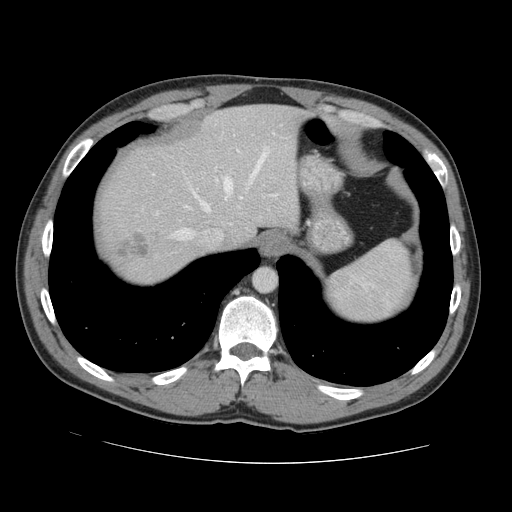
Contrast-enhanced abdominal CT, one axial slice. Intravenous contrast given. Soft-tissue window (W 400 / L 40 HU). 2.5 mm slice thickness. 512 × 512 image matrix, field of view 380 × 380 mm. Male patient, age 40 years. From the clinical record (not read from this slice): diagnosis: colorectal cancer liver metastases, imaged before liver resection; multiple liver metastases: yes; largest metastasis: 2.9 cm; disease in both lobes: yes.
Annotated regions visible in this slice (expert manual segmentation):
- hepatic veins: bounding box <175,152,267,240> (left, top, right, bottom; pixels)
- liver: <97,105,302,283>
- planned liver remnant (the part of the liver to remain after resection): <115,105,302,245>
- liver metastasis: <116,231,159,258>